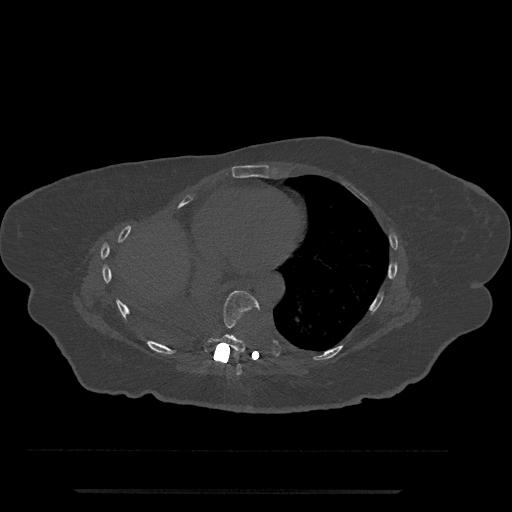
CT including the spine, one axial slice; slice 392 of 797 in the series (ordered by position); bone window (W 1800 / L 400 HU); 512 × 512 image matrix. Patient: female, 51 years. From the clinical record (not read from this slice): primary cancer: neuro.
Structures marked on this image (semi-automatically segmented with operator editing):
- T7 vertebra: box from (x=233, y=364) to (x=242, y=376) px
- T8 vertebra: (x=203, y=291)–(x=260, y=352)